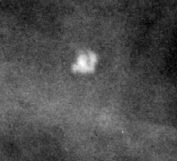
Crop from a digitized film mammogram around one marked abnormality, right breast, CC view, BI-RADS breast density category 3 (scale 1–4).
Finding: calcifications, morphology lucent center; BI-RADS assessment category 2; benign without callback (not worked up further).